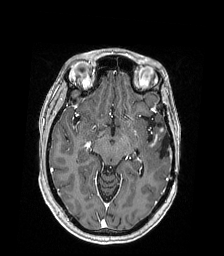
Brain MRI from a brain-tumour surgery series, one axial slice. Position 111 of 168 along the scan axis. T1-weighted post-contrast. 1 mm slice thickness. 224 × 256 image matrix, field of view 224 × 256 mm. Case-level facts recorded for this patient, not image findings: histopathology: Astrocytoma; WHO grade: 4; IDH mutation: yes; tumour location: Left Temporal.
Outlined on this slice (manually delineated by an expert):
- tumour: box from (x=153, y=125) to (x=165, y=146) px